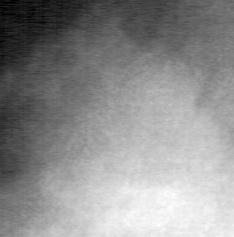
Region of interest cut from a scanned film mammogram (one marked finding), left breast, CC view.
Finding: mass, shape oval, margins ill defined; BI-RADS assessment category 4; subtlety rating 3 on a 1 (subtle) to 5 (obvious) scale; pathology result (as recorded, not read from the image): benign.